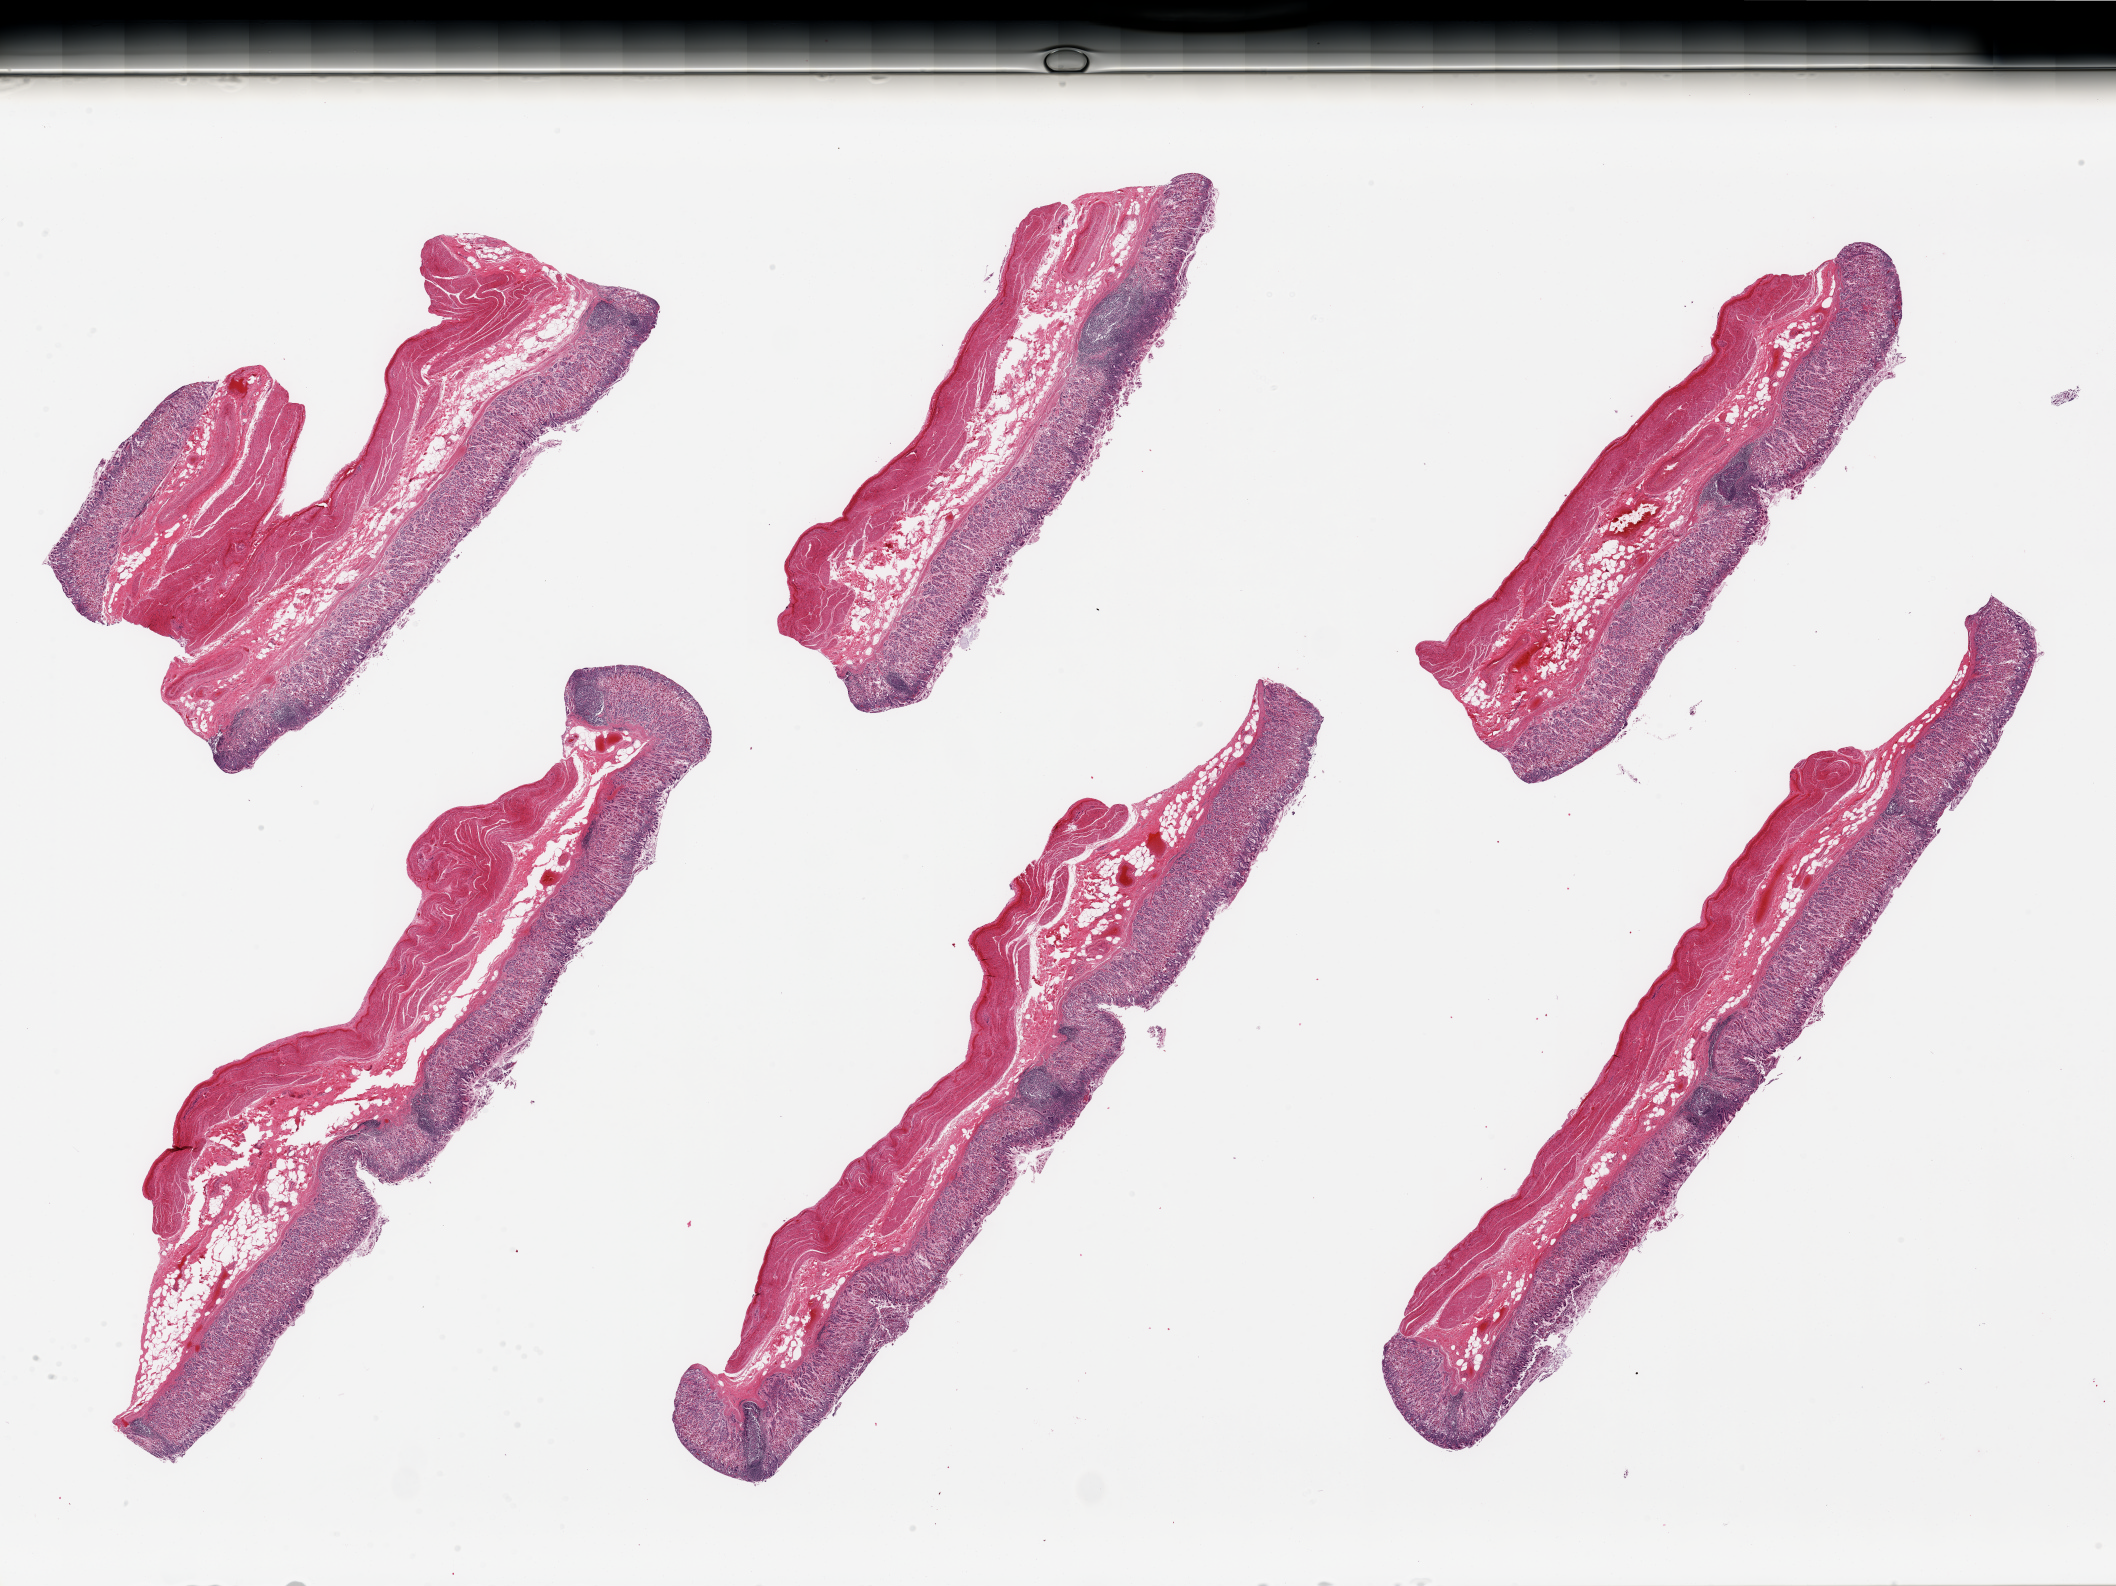
H&E whole-slide image, a low-resolution overview of the entire scanned area, about 33.5 x 25.1 mm (slide scanned at 20x), PAXgene-fixed paraffin-embedded (PFPE) section, sampled site (target tissue): stomach, donor tissue sample. Male donor.
Reviewer comment on this tissue sample: 6 pieces, target mucosa up to ~0.9 mm, 30-50% of thickness. Chronic gastritis; pattern suggests H pylori.